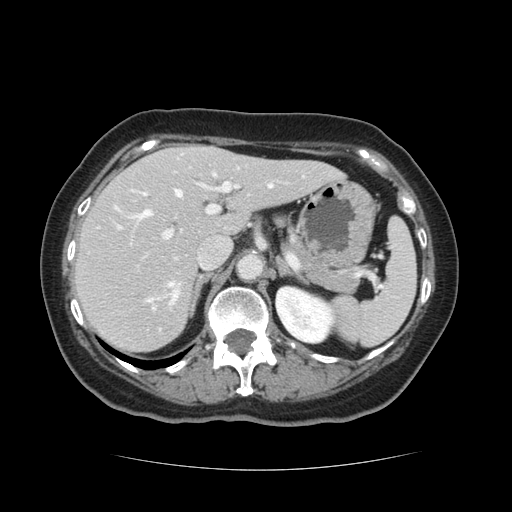
Contrast-enhanced abdominal CT, one axial slice. Position 79 of 128 along the scan axis. 120 kVp. Intravenous contrast given. Soft-tissue window (W 400 / L 40 HU). 2.5 mm slice thickness. 512 × 512 image matrix, field of view 366 × 366 mm. Female patient, age 67 years. From the clinical record (not read from this slice): diagnosis: colorectal cancer liver metastases, imaged before liver resection; multiple liver metastases: yes; largest metastasis: 3 cm; disease in both lobes: yes.
Annotated regions visible in this slice (manually delineated by an expert):
- hepatic veins: bounding box (x1, y1, x2, y2) in pixels: (139, 185, 273, 305)
- liver: (74, 146, 339, 352)
- planned liver remnant (the part of the liver to remain after resection): (74, 158, 339, 352)
- portal vein (with intrahepatic branches): (117, 171, 238, 308)